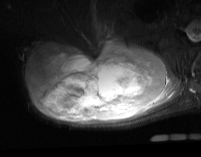
MRI of an extremity soft-tissue mass, one axial slice. Position 41 of 74 along the scan axis. STIR. MR volume resampled by the dataset authors to the PET/CT grid (not the native acquisition matrix). 3.27 mm slice thickness. 201 × 157 image matrix, field of view 196 × 153 mm. Male patient. From the clinical record (not read from this slice): histological type: pleiomorphic spindle cell undifferentiated; grade: high; site of the primary tumour: right parascapusular.
Outlined on this slice (expert contour drawn on MRI and transferred to this co-registered scan by the dataset authors):
- gross tumour volume including surrounding oedema: bounding box <26,36,180,124> (left, top, right, bottom; pixels)
- gross tumour volume (mass): <28,41,168,122>